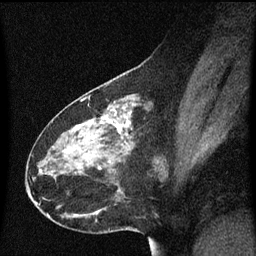
Breast MRI (dynamic contrast-enhanced), one sagittal slice; dynamic contrast-enhanced series, image 2 of 3 at this slice position (ordered by acquisition); 1.5 T; TE 4.2 ms, TR 8.4 ms; 2 mm slice thickness; 256 × 256 image matrix, field of view 200 × 200 mm. Patient: female, 49 years. From the clinical record (not read from this slice): setting: breast cancer imaged before/during neoadjuvant chemotherapy; receptor status: HR-positive, HER2-negative.
Outlined on this slice (semi-automatic segmentation, software-assisted and operator-edited):
- analysis volume of interest (the breast-tissue region the enhancement analysis was run in; not a lesion): box from (x=27, y=96) to (x=170, y=221) px
- tumour enhancement mask (voxels above the 70 % enhancement threshold inside the analysis volume of interest): (x=106, y=116)–(x=129, y=163)